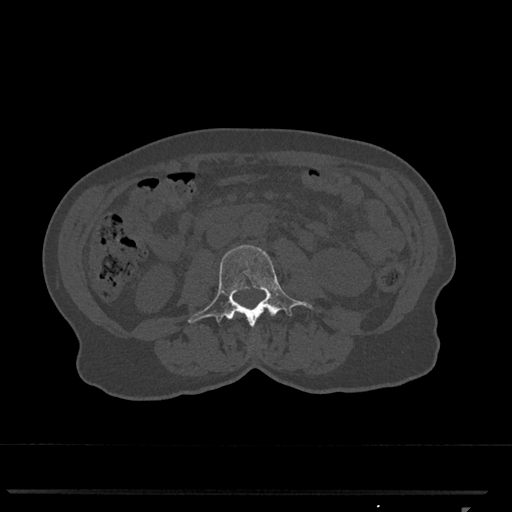
CT including the spine, one axial slice; position 279 of 793 along the scan axis; reconstruction kernel Br40s/3; 120 kVp; bone window (W 1800 / L 400 HU); 0.5 mm slice thickness; 512 × 512 image matrix. Patient: female, 62 years. Case-level facts recorded for this patient, not image findings: primary cancer: renal.
Outlined on this slice (semi-automatically segmented with operator editing):
- L2 vertebra: box from (x=235, y=314) to (x=237, y=317) px
- L3 vertebra: (x=188, y=245)–(x=313, y=327)